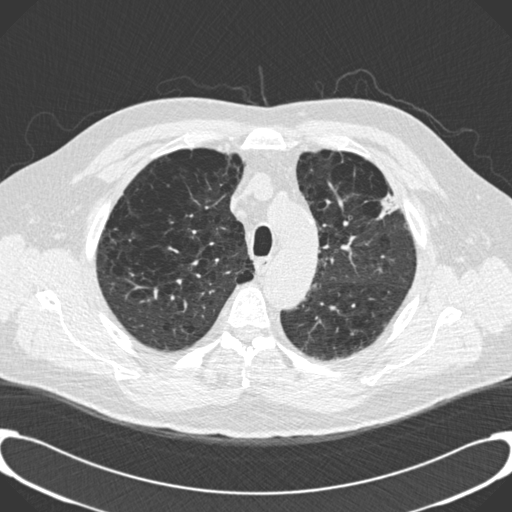
Low-dose screening chest CT, one axial slice. Position 152 of 189 along the scan axis. Reconstruction kernel B30f. Lung window (W 1500 / L -600 HU). 2 mm slice thickness. 512 × 512 image matrix, field of view 380 × 380 mm.
Annotated regions visible in this slice (outlined manually by an expert reader):
- lesion 1 (tumor, upper lobe of left lung): box from (x=378, y=193) to (x=401, y=219) px